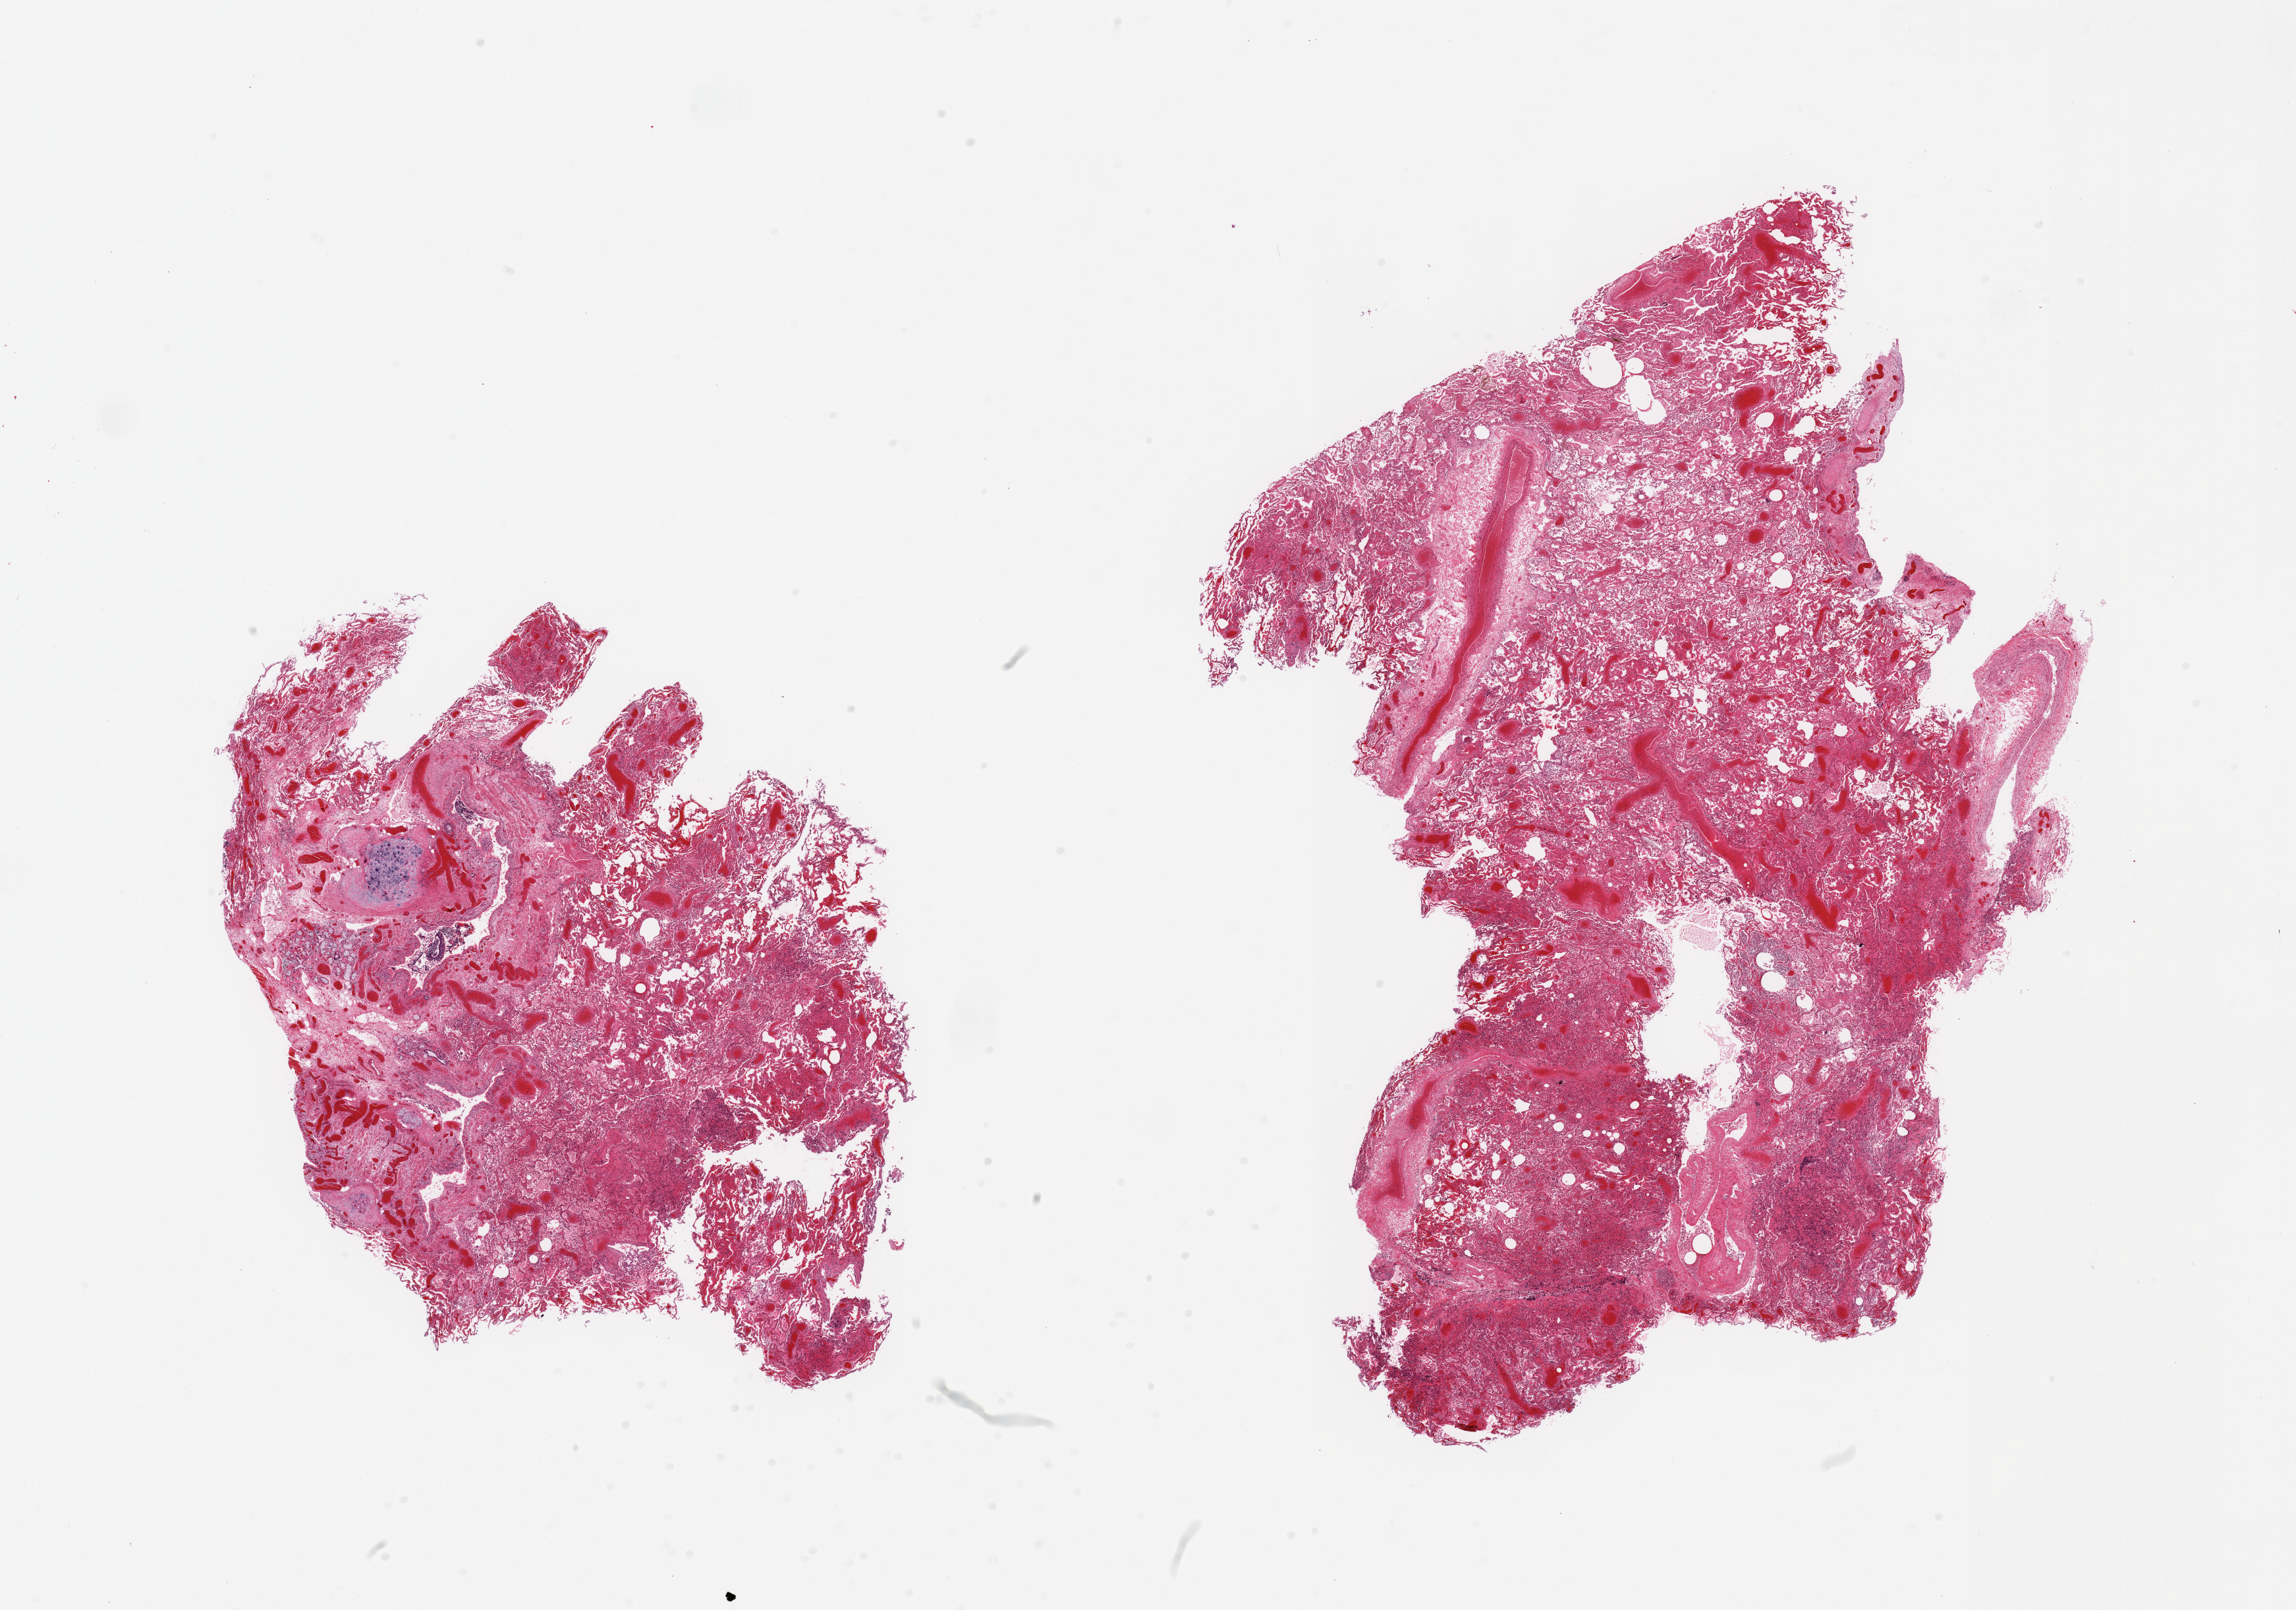
Hematoxylin and eosin (H&E) whole-slide image, low-resolution overview of the scanned area, about 27.6 x 19.3 mm (from a 20x scan); PAXgene-fixed paraffin-embedded (PFPE) section; sampled site (target tissue): lung; tissue donor sample. Donor sex: female.
Reviewer comment on this tissue sample: 2 pieces, moderate acute congestion, moderate diffuse acute pneumonitis/edema.